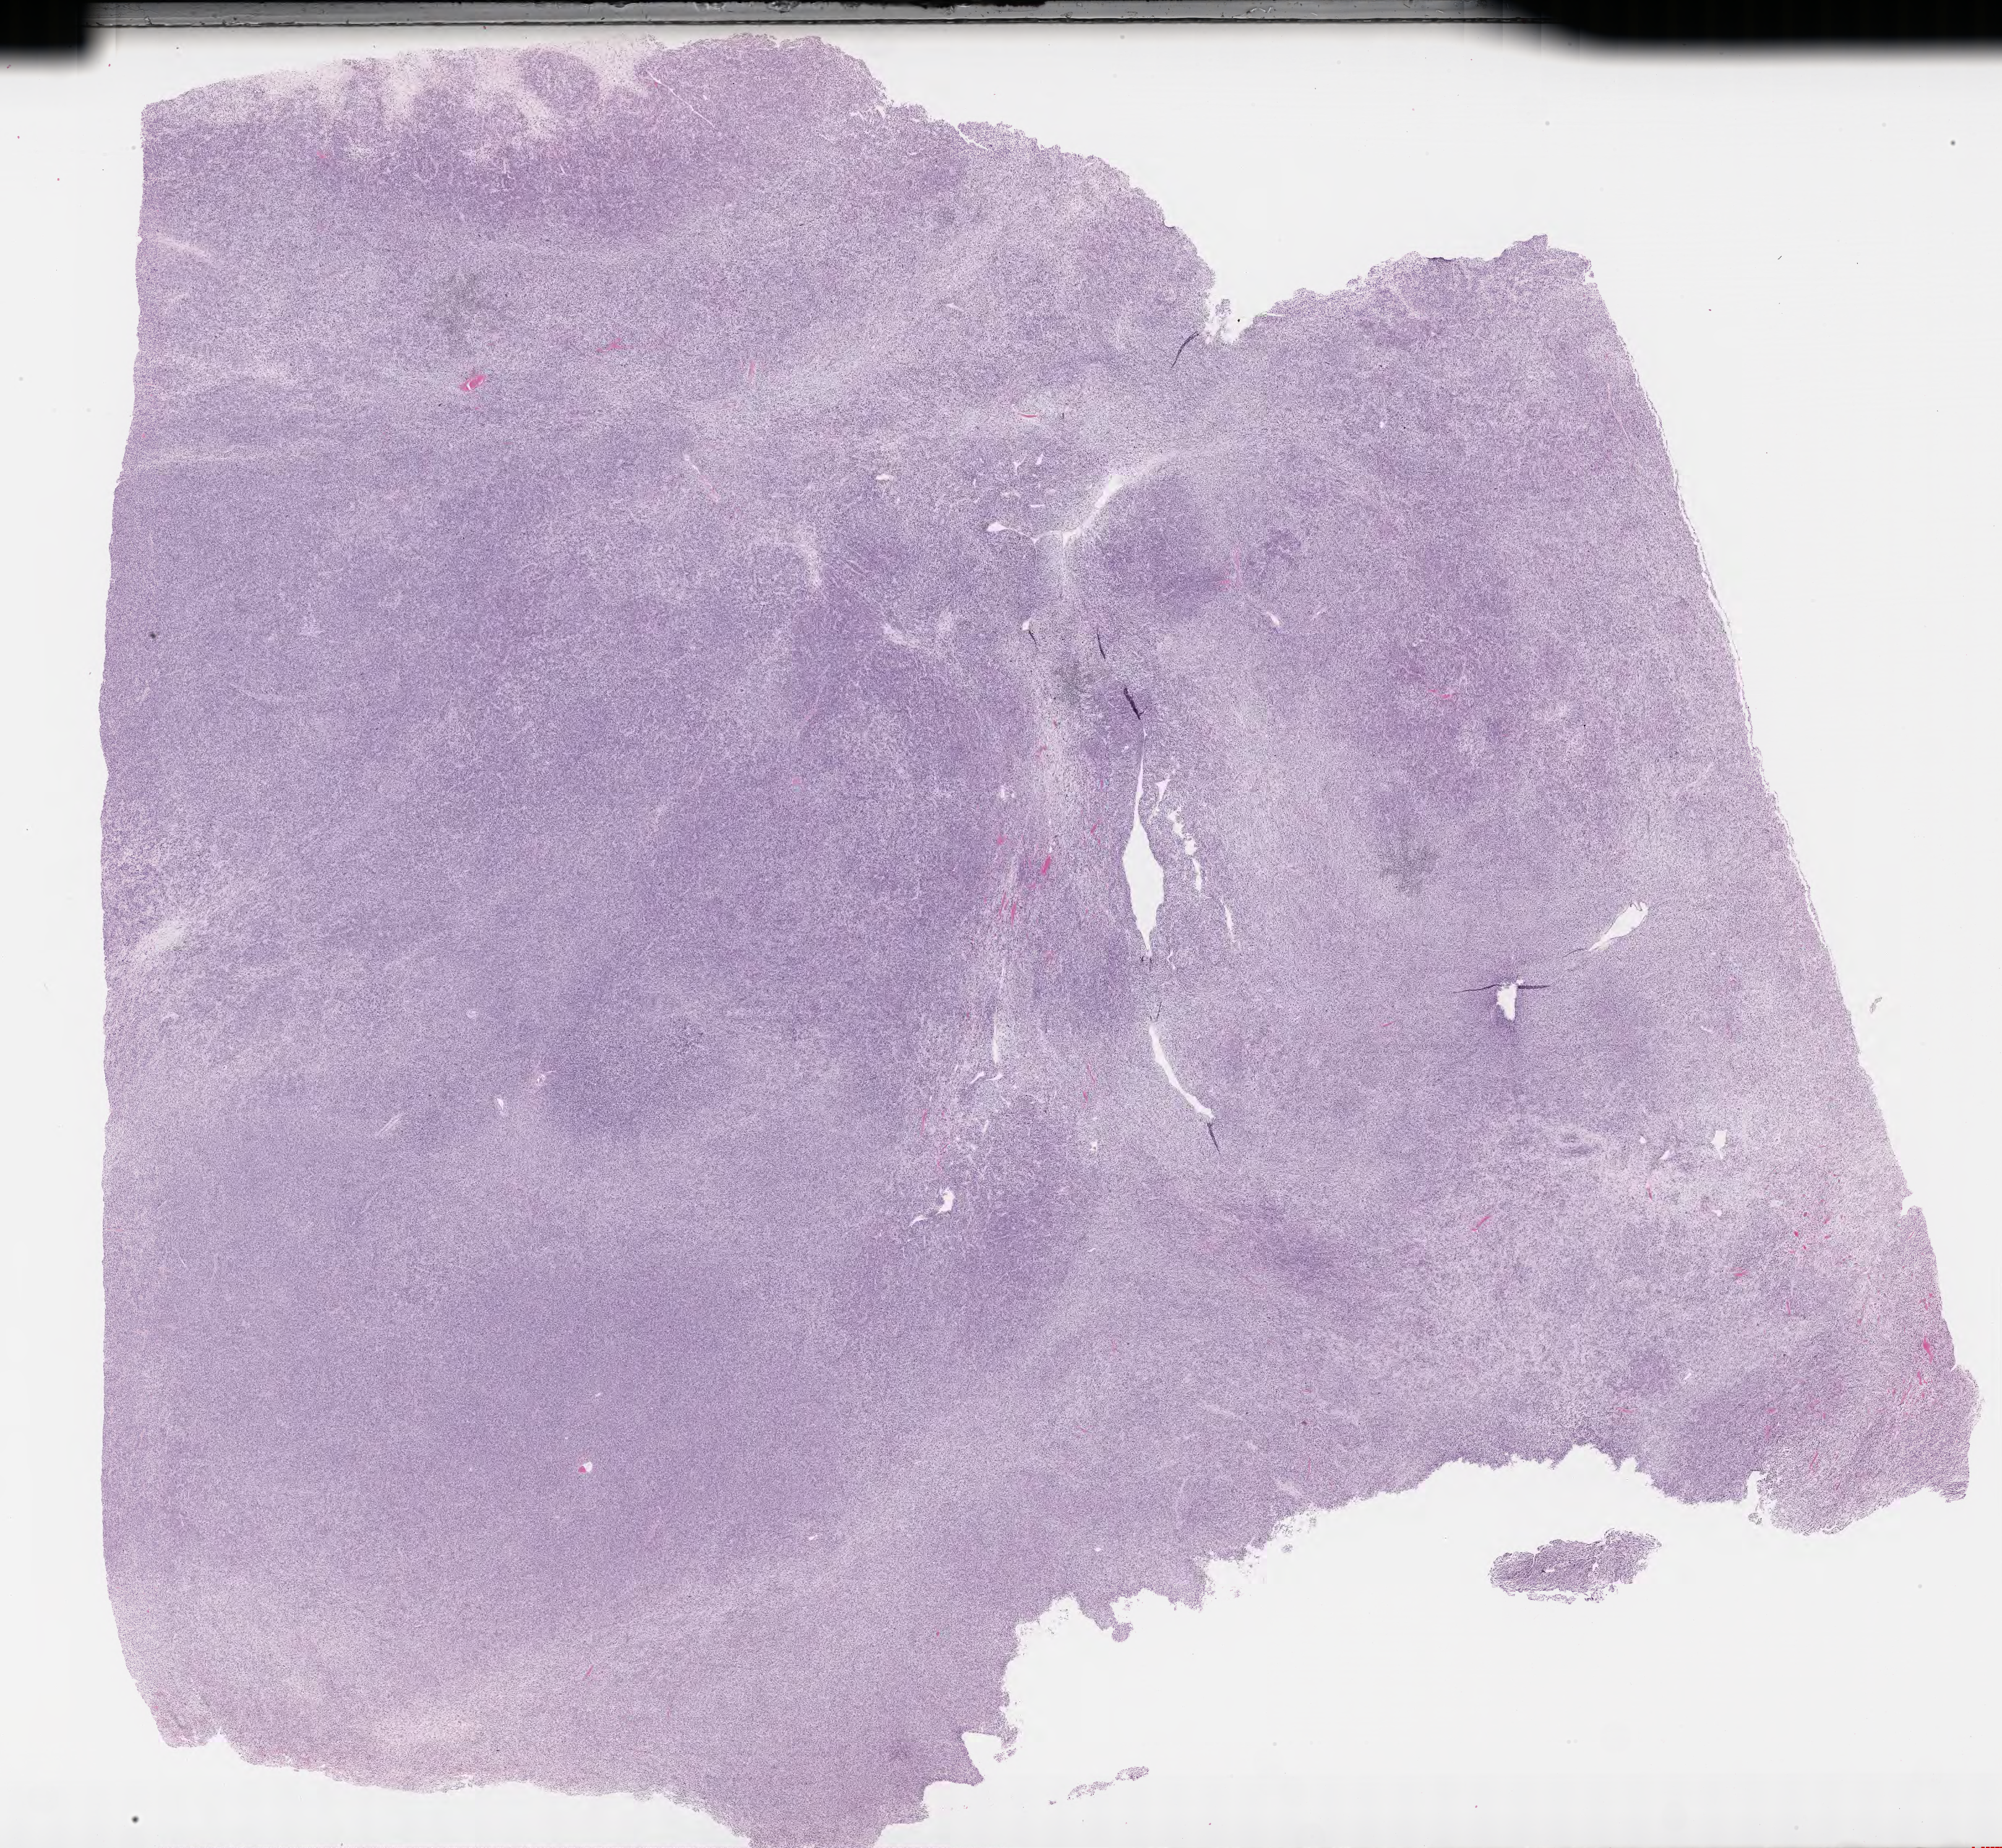
H&E whole-slide image of tumor tissue — shown as a low-resolution overview of the whole scanned area (about 26.2 x 24.2 mm), formalin-fixed, paraffin-embedded (FFPE) tissue, sample anatomic site: testicle-left. Patient: male, age 14.5 years at diagnosis.
Stage (as recorded): 1. Primary site (case record): testis-paratesticular. Metastatic status at presentation (as recorded): non-metastatic (unconfirmed). Diagnosis: rhabdomyosarcoma; histological classification: embryonal rhabdomyosarcoma.